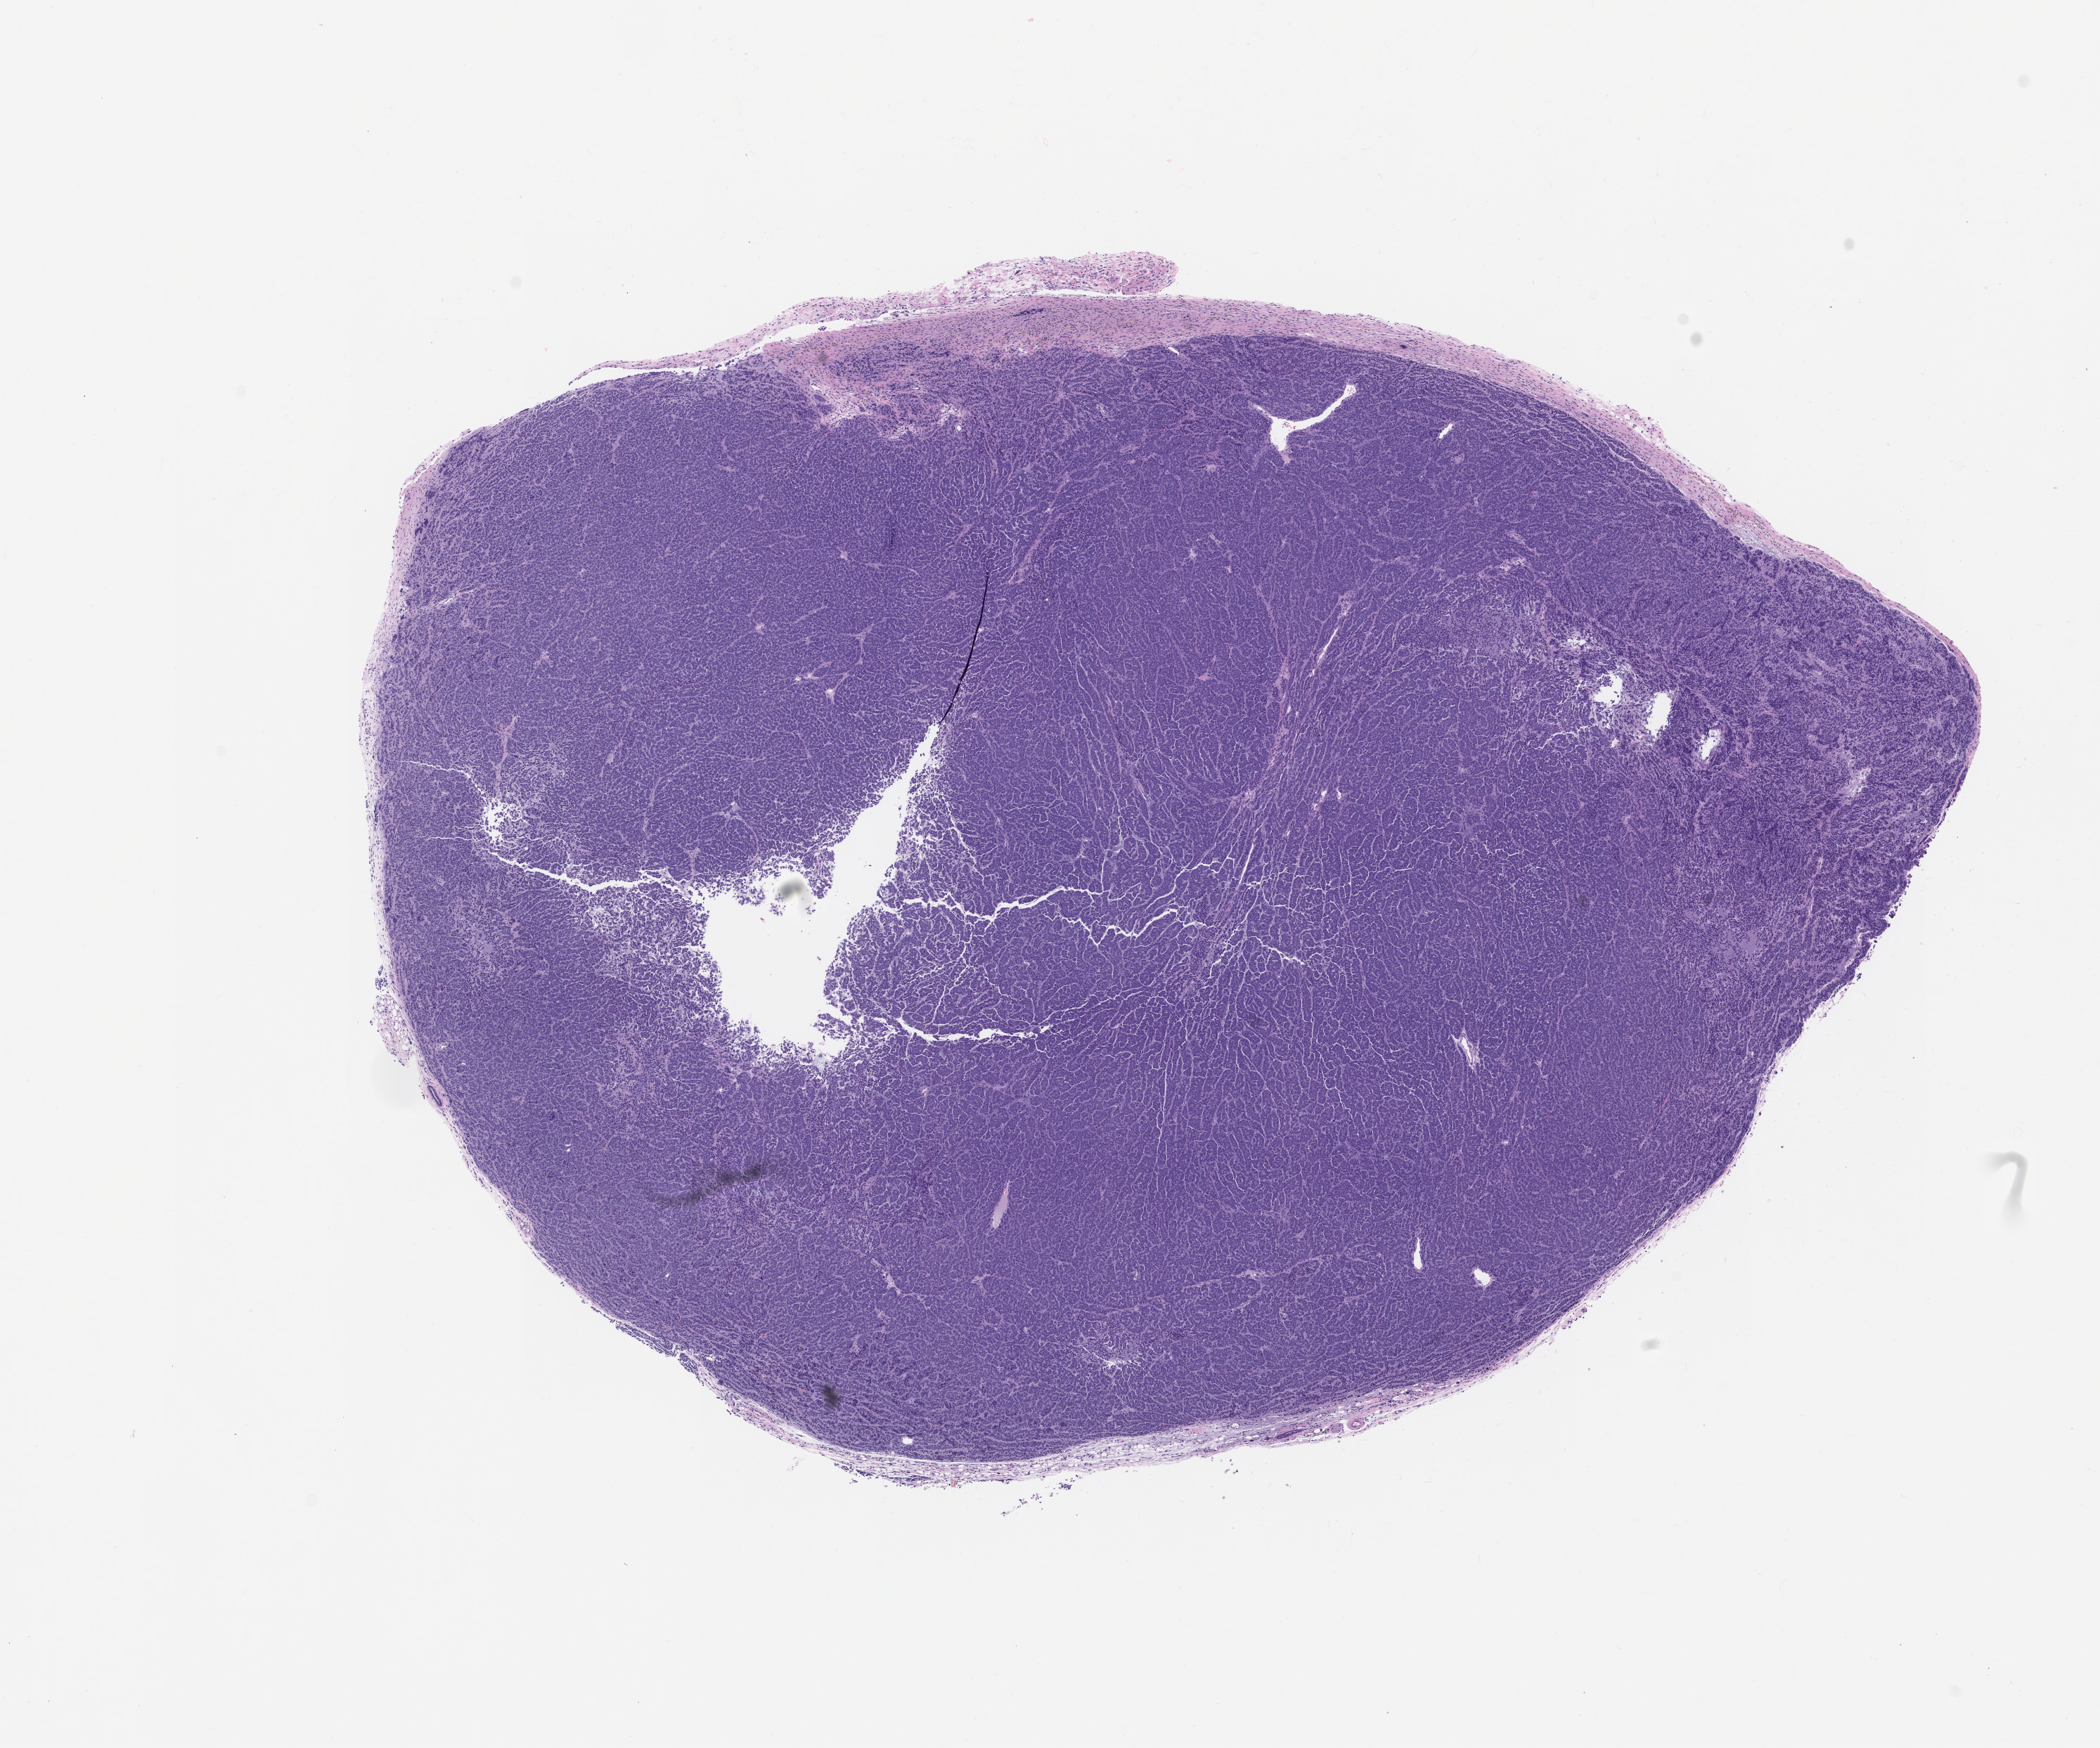
Hematoxylin and eosin (H&E) whole-slide image of a patient-derived xenograft (PDX) tumor grown in a mouse, passage 0, a low-resolution overview of the entire scanned area, about 12.0 x 10.0 mm; FFPE section; tumor site category: ovary.
Originating patient diagnosis: Ovarian Carcinoma.